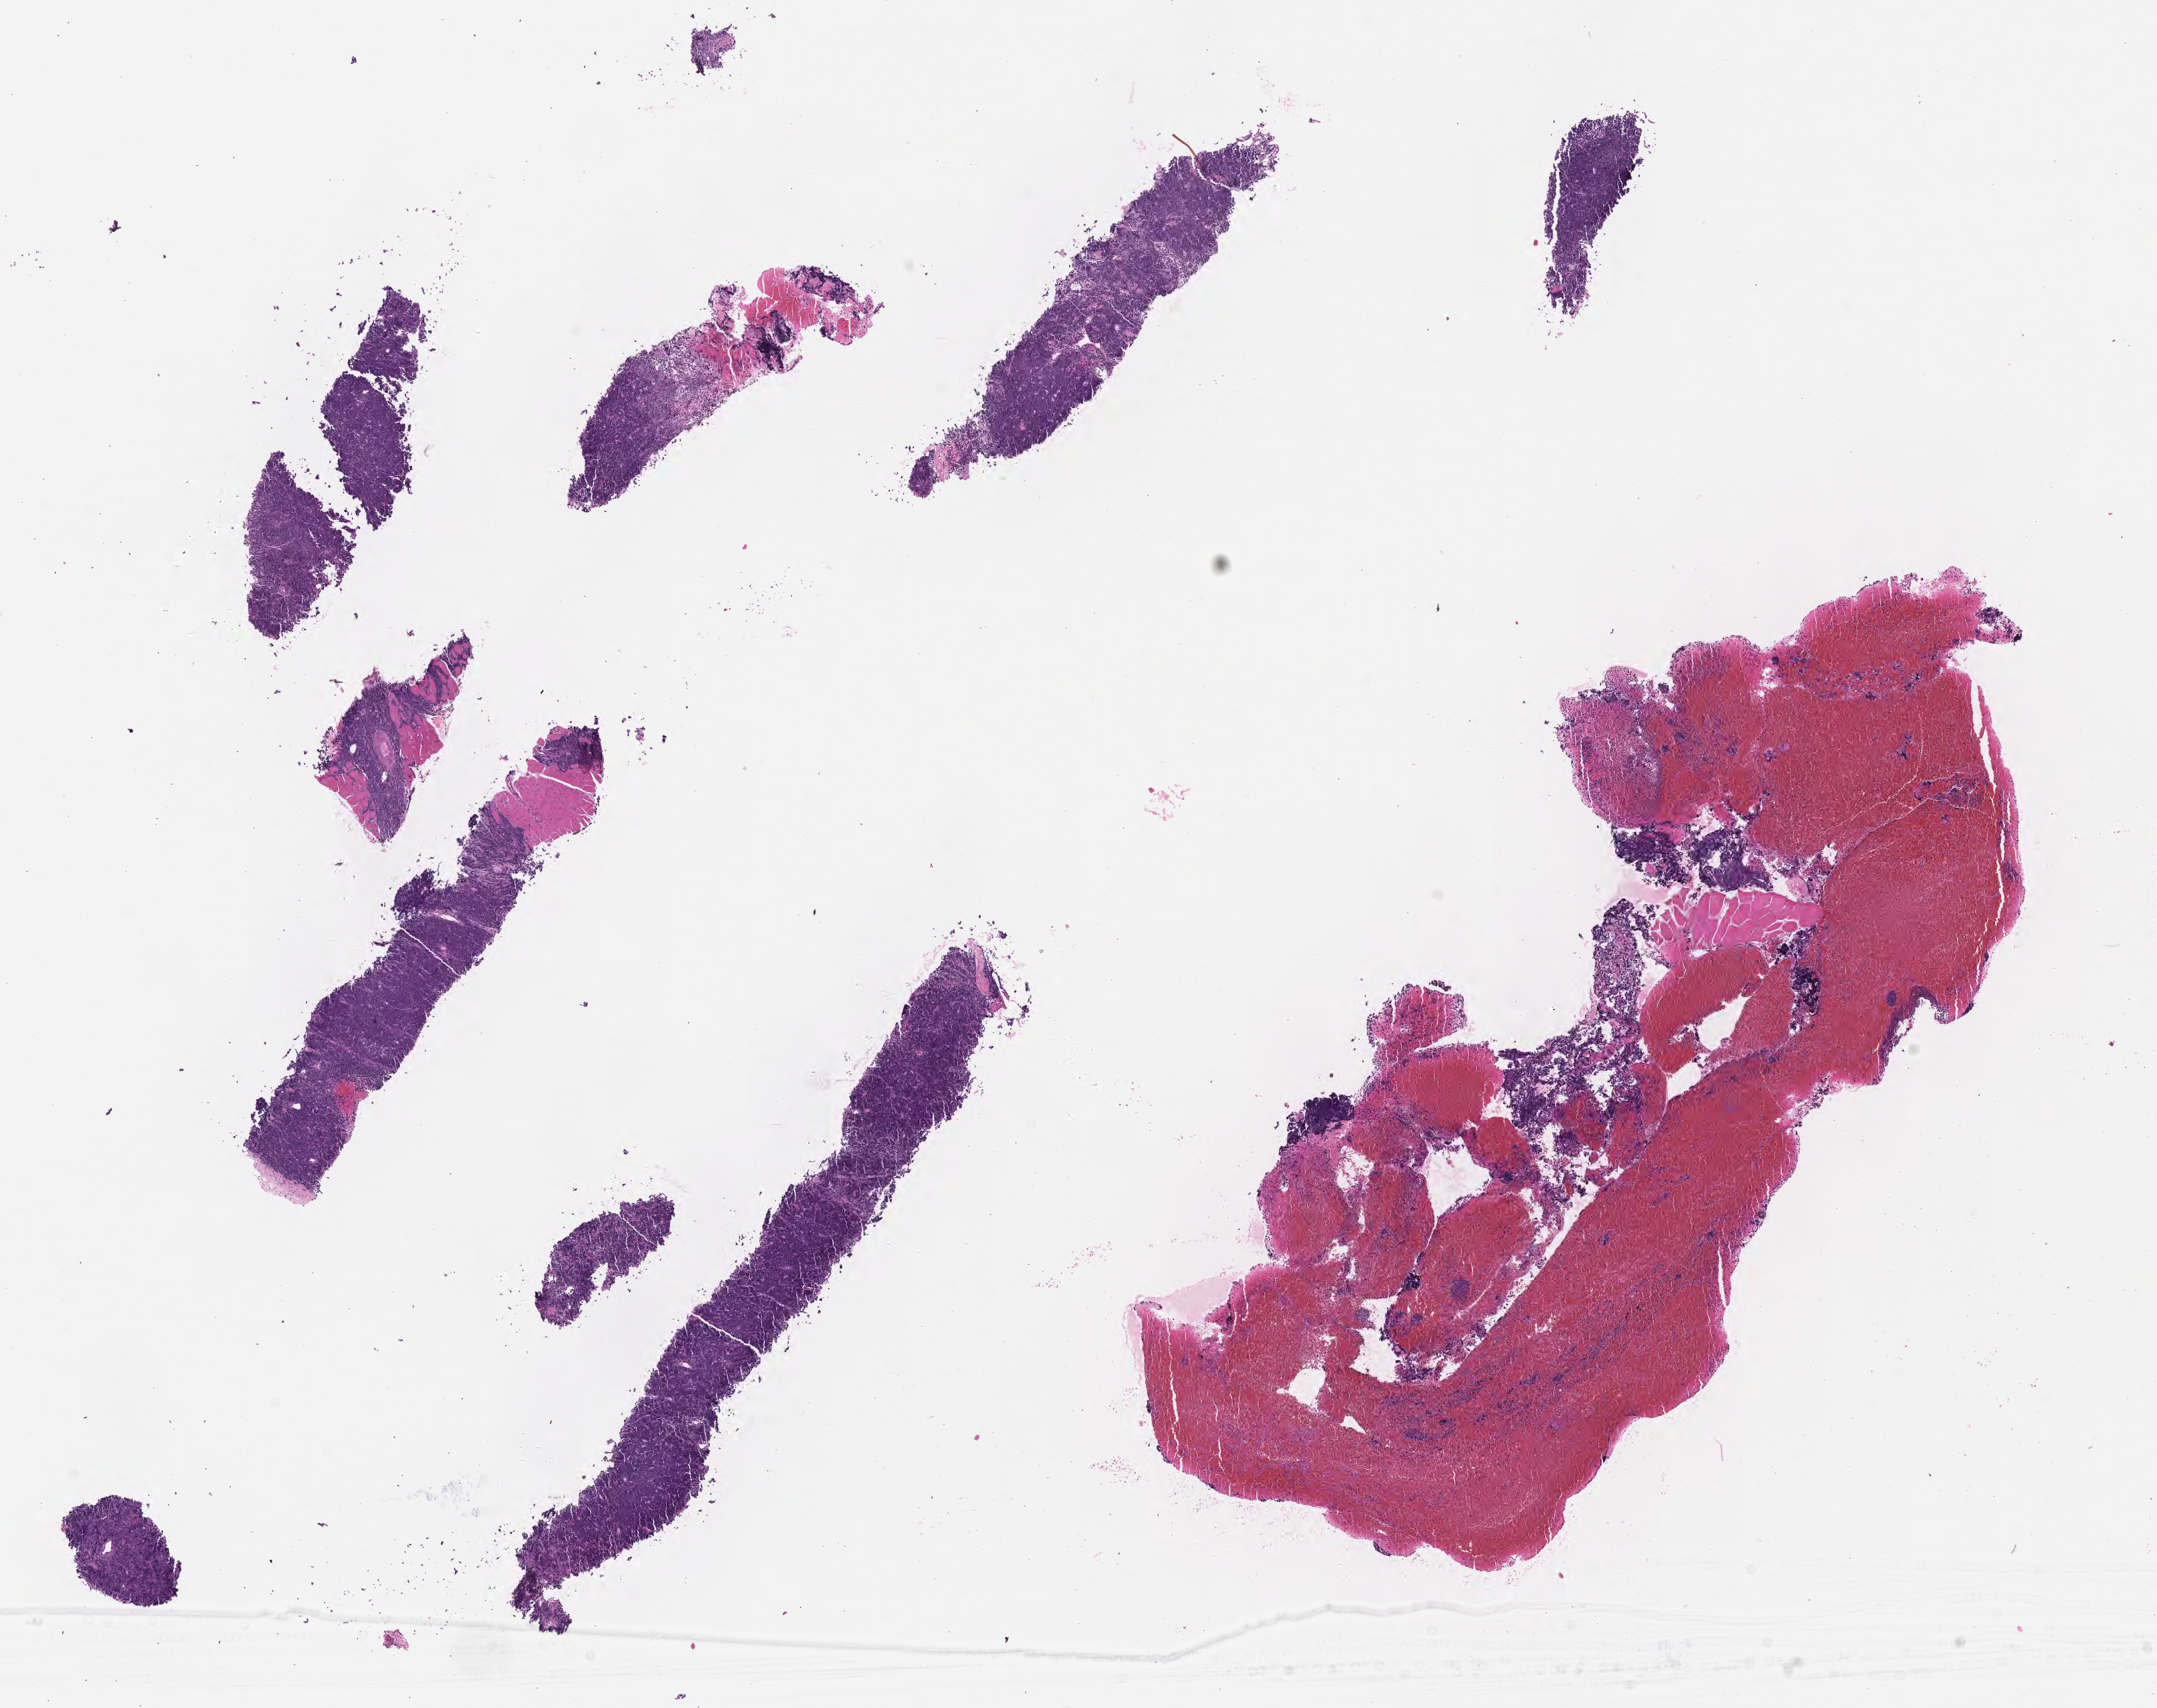
Whole-slide image, haematoxylin and eosin stain — low-resolution overview of the scanned area, about 13.1 x 10.4 mm; formalin-fixed paraffin-embedded section; specimen: primary tumor. Male patient, age 29 years. Pathologist review of this section (percent, as recorded): tumor cells 40%, tumor nuclei 85%, stromal cells 10%, necrosis 50%, normal cells 0%. Inflammatory infiltration, as recorded: lymphocyte infiltration 40%, monocyte infiltration 15%, neutrophil infiltration 5%.
Ann Arbor stage (patient): Stage IV. Section: top of the tissue portion. Diagnosis: Burkitt lymphoma, NOS.